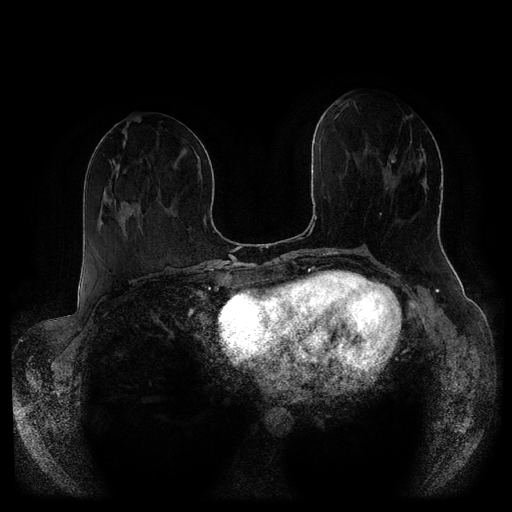
Breast MRI (dynamic contrast-enhanced, multi-phase), one axial slice; slice 39 of 116 in the series (ordered by position); dynamic contrast-enhanced series, time point 2 of 5 at this slice position (early post-contrast); 1.5 T; TE 2.6 ms, TR 5.3 ms; 2 mm slice thickness; 512 × 512 image matrix. Patient: female, 51 years.
Annotated regions visible in this slice (semi-automatic segmentation, software-assisted and operator-edited):
- breast lesion (labelled 'tumour' in the annotation; benign lesions carry a separate 'benign' label): bounding box <388,152,397,175> (left, top, right, bottom; pixels)